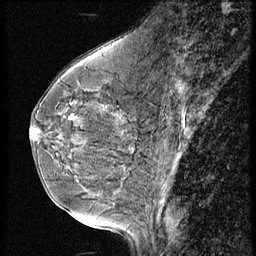
Breast MRI (dynamic contrast-enhanced), one sagittal slice. 3 images stored at this slice position (order not interpretable as contrast timing). 1.5 T. TE 4.2 ms, TR 9 ms. 2.5 mm slice thickness. 256 × 256 image matrix. Female patient, age 49 years. From the clinical record (not read from this slice): setting: breast cancer imaged before/during neoadjuvant chemotherapy; receptor status: HER2-positive.
Structures marked on this image (semi-automatic segmentation, software-assisted and operator-edited):
- analysis volume of interest (the breast-tissue region the enhancement analysis was run in; not a lesion): bounding box [x1, y1, x2, y2] px = [30, 75, 128, 193]
- tumour enhancement mask (voxels above the 140 % enhancement threshold inside the analysis volume of interest): [32, 130, 36, 135]